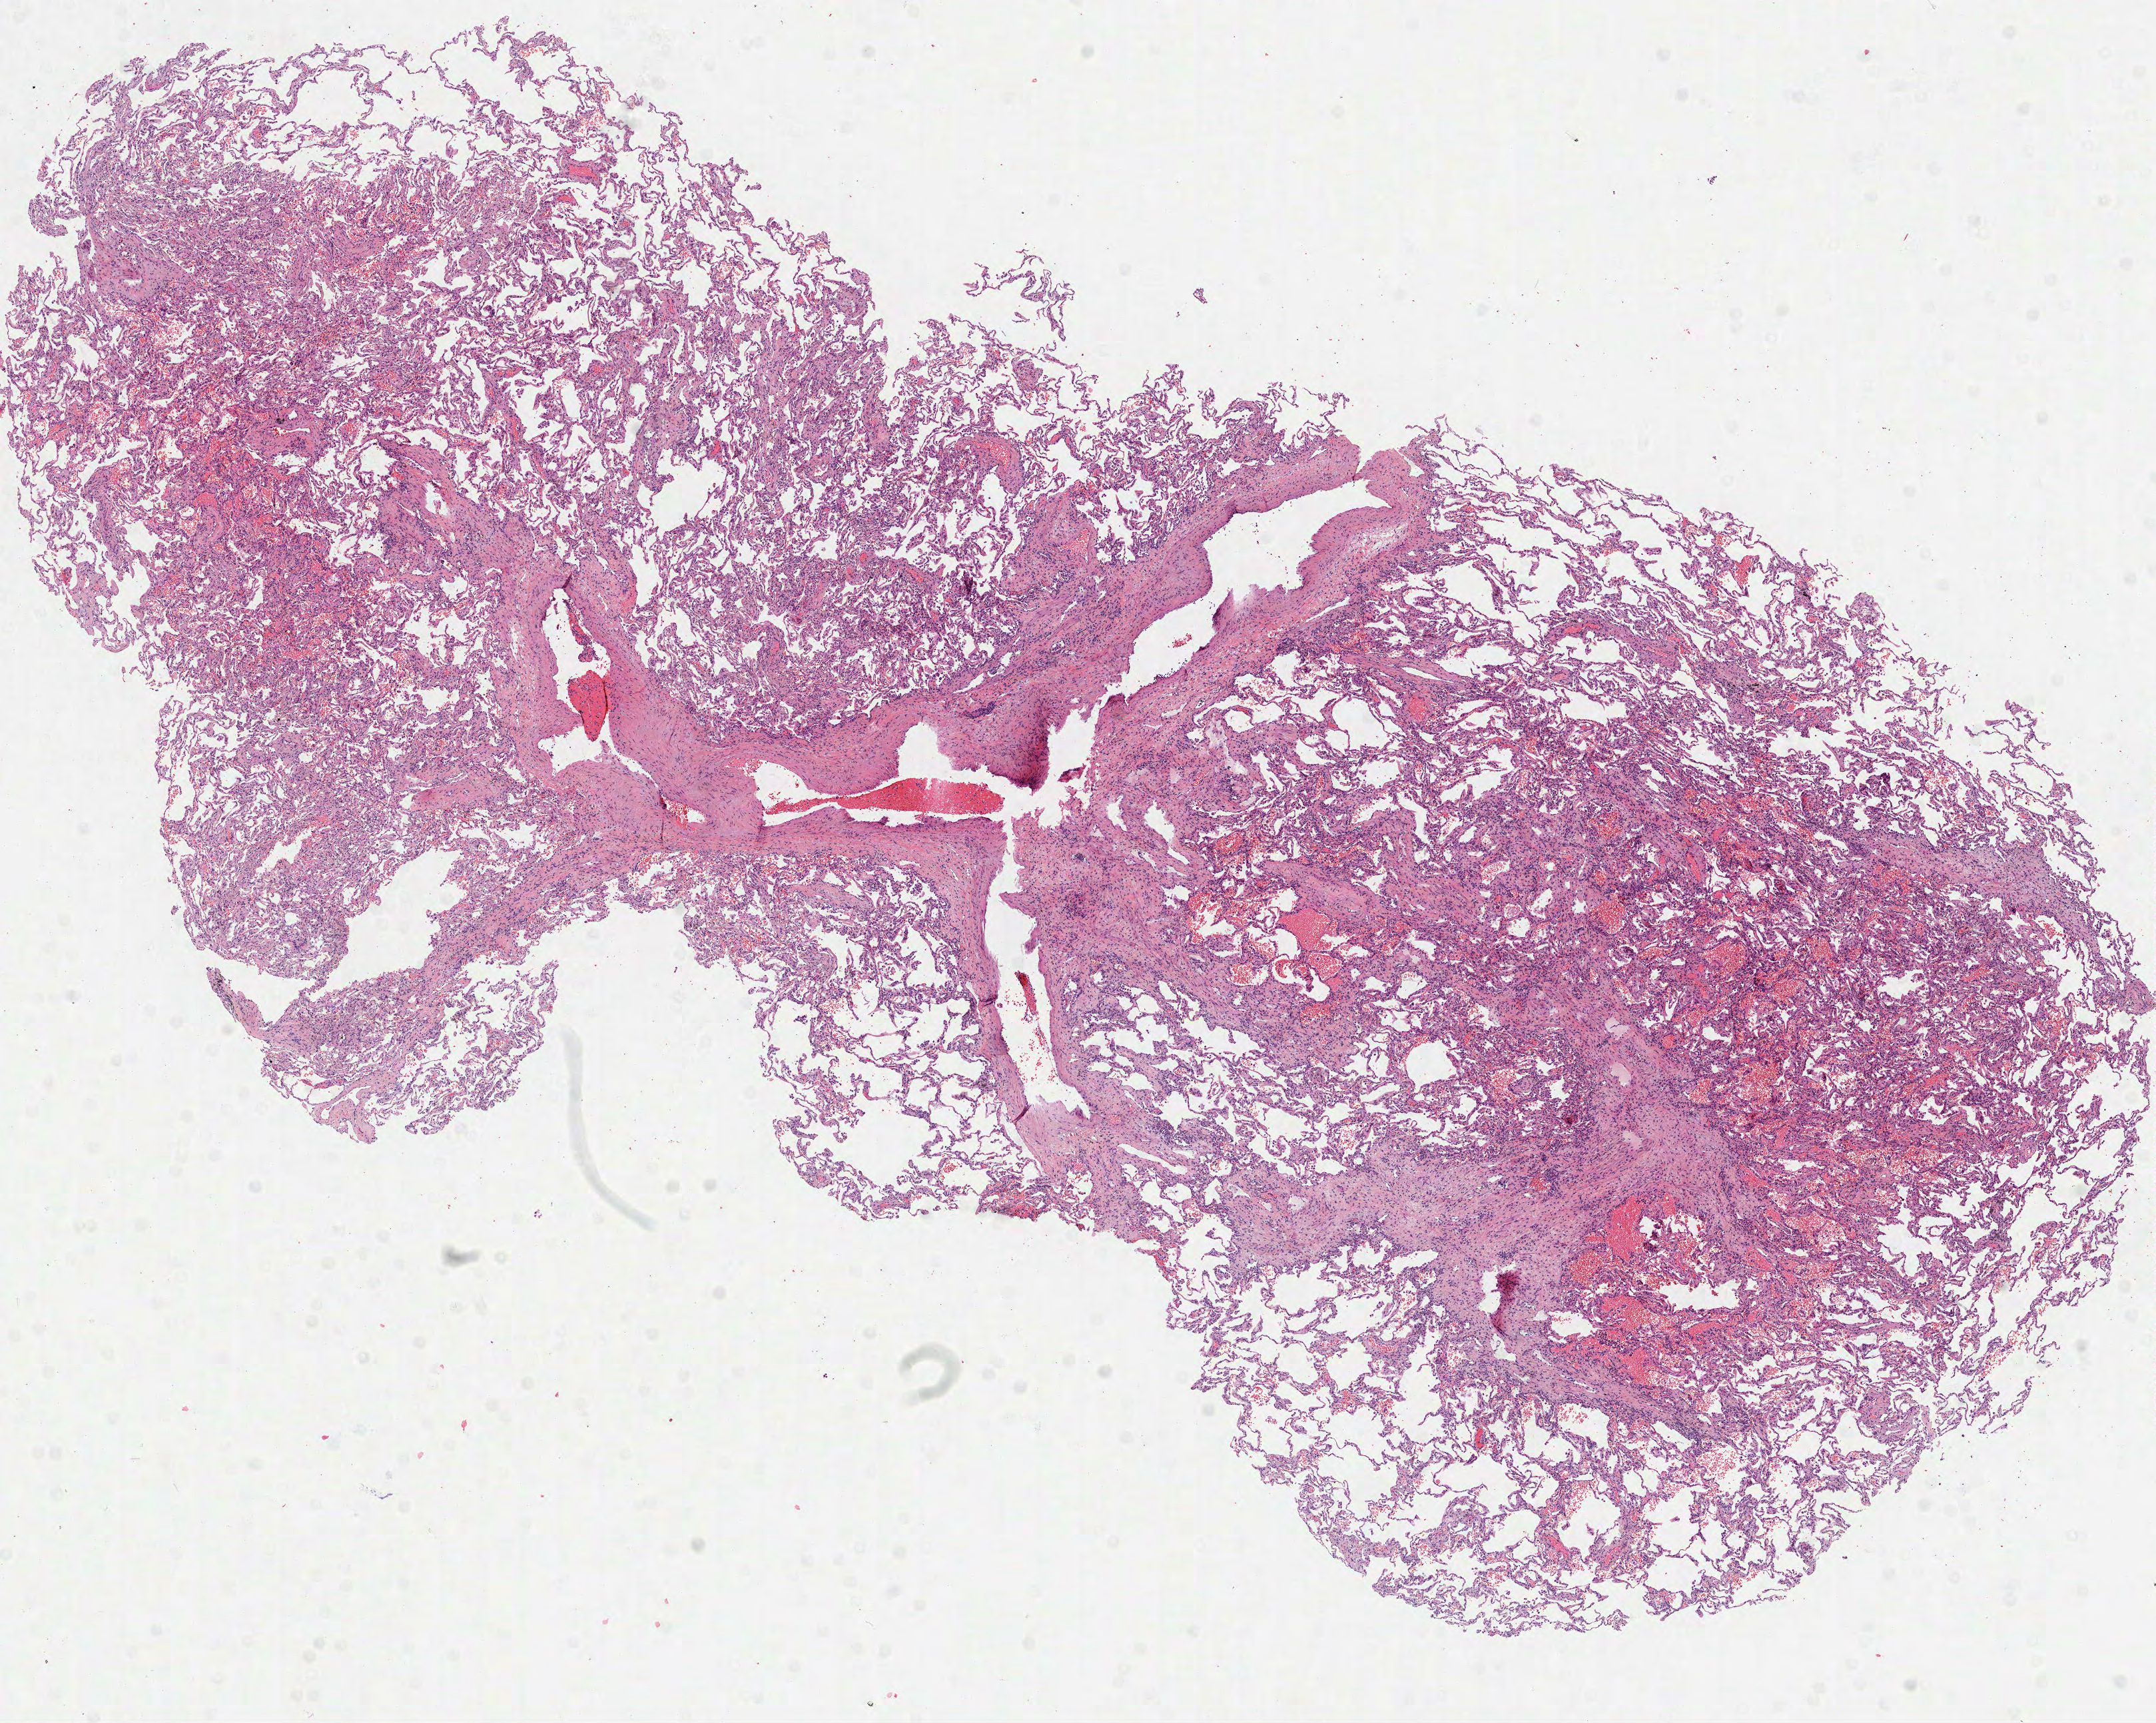
Digitized H&E-stained tissue section (whole slide), whole scanned area (about 13.1 x 10.4 mm, from a 40x scan) shown as a low-resolution overview. Frozen section from the top of the tissue portion. Lung, solid tissue normal (non-tumour tissue) sample. Male patient; age at initial diagnosis 56 years. Infiltration values recorded for this section: lymphocyte infiltration 0%, monocyte infiltration 10%, neutrophil infiltration 0%.
This section: solid tissue normal sample (biorepository sample class). Patient diagnosis: Squamous cell carcinoma, NOS (upper lobe, lung).